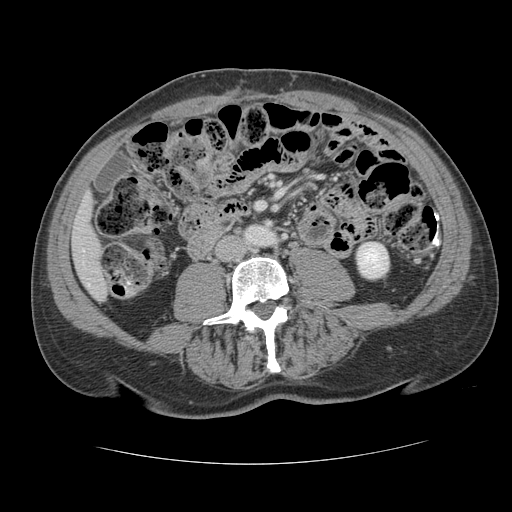
Contrast-enhanced abdominal CT, one axial slice; slice 25 of 134 in the series (ordered by position); 120 kVp; intravenous contrast given; soft-tissue window (W 400 / L 40 HU); 2.5 mm slice thickness; 512 × 512 image matrix, field of view 377 × 377 mm. Male patient, age 68 years. From the clinical record (not read from this slice): diagnosis: colorectal cancer liver metastases, imaged before liver resection; multiple liver metastases: yes; largest metastasis: 2.2 cm; disease in both lobes: no.
Outlined on this slice (expert manual segmentation):
- liver: bounding box <73,199,108,299> (left, top, right, bottom; pixels)
- planned liver remnant (the part of the liver to remain after resection): <73,200,108,299>